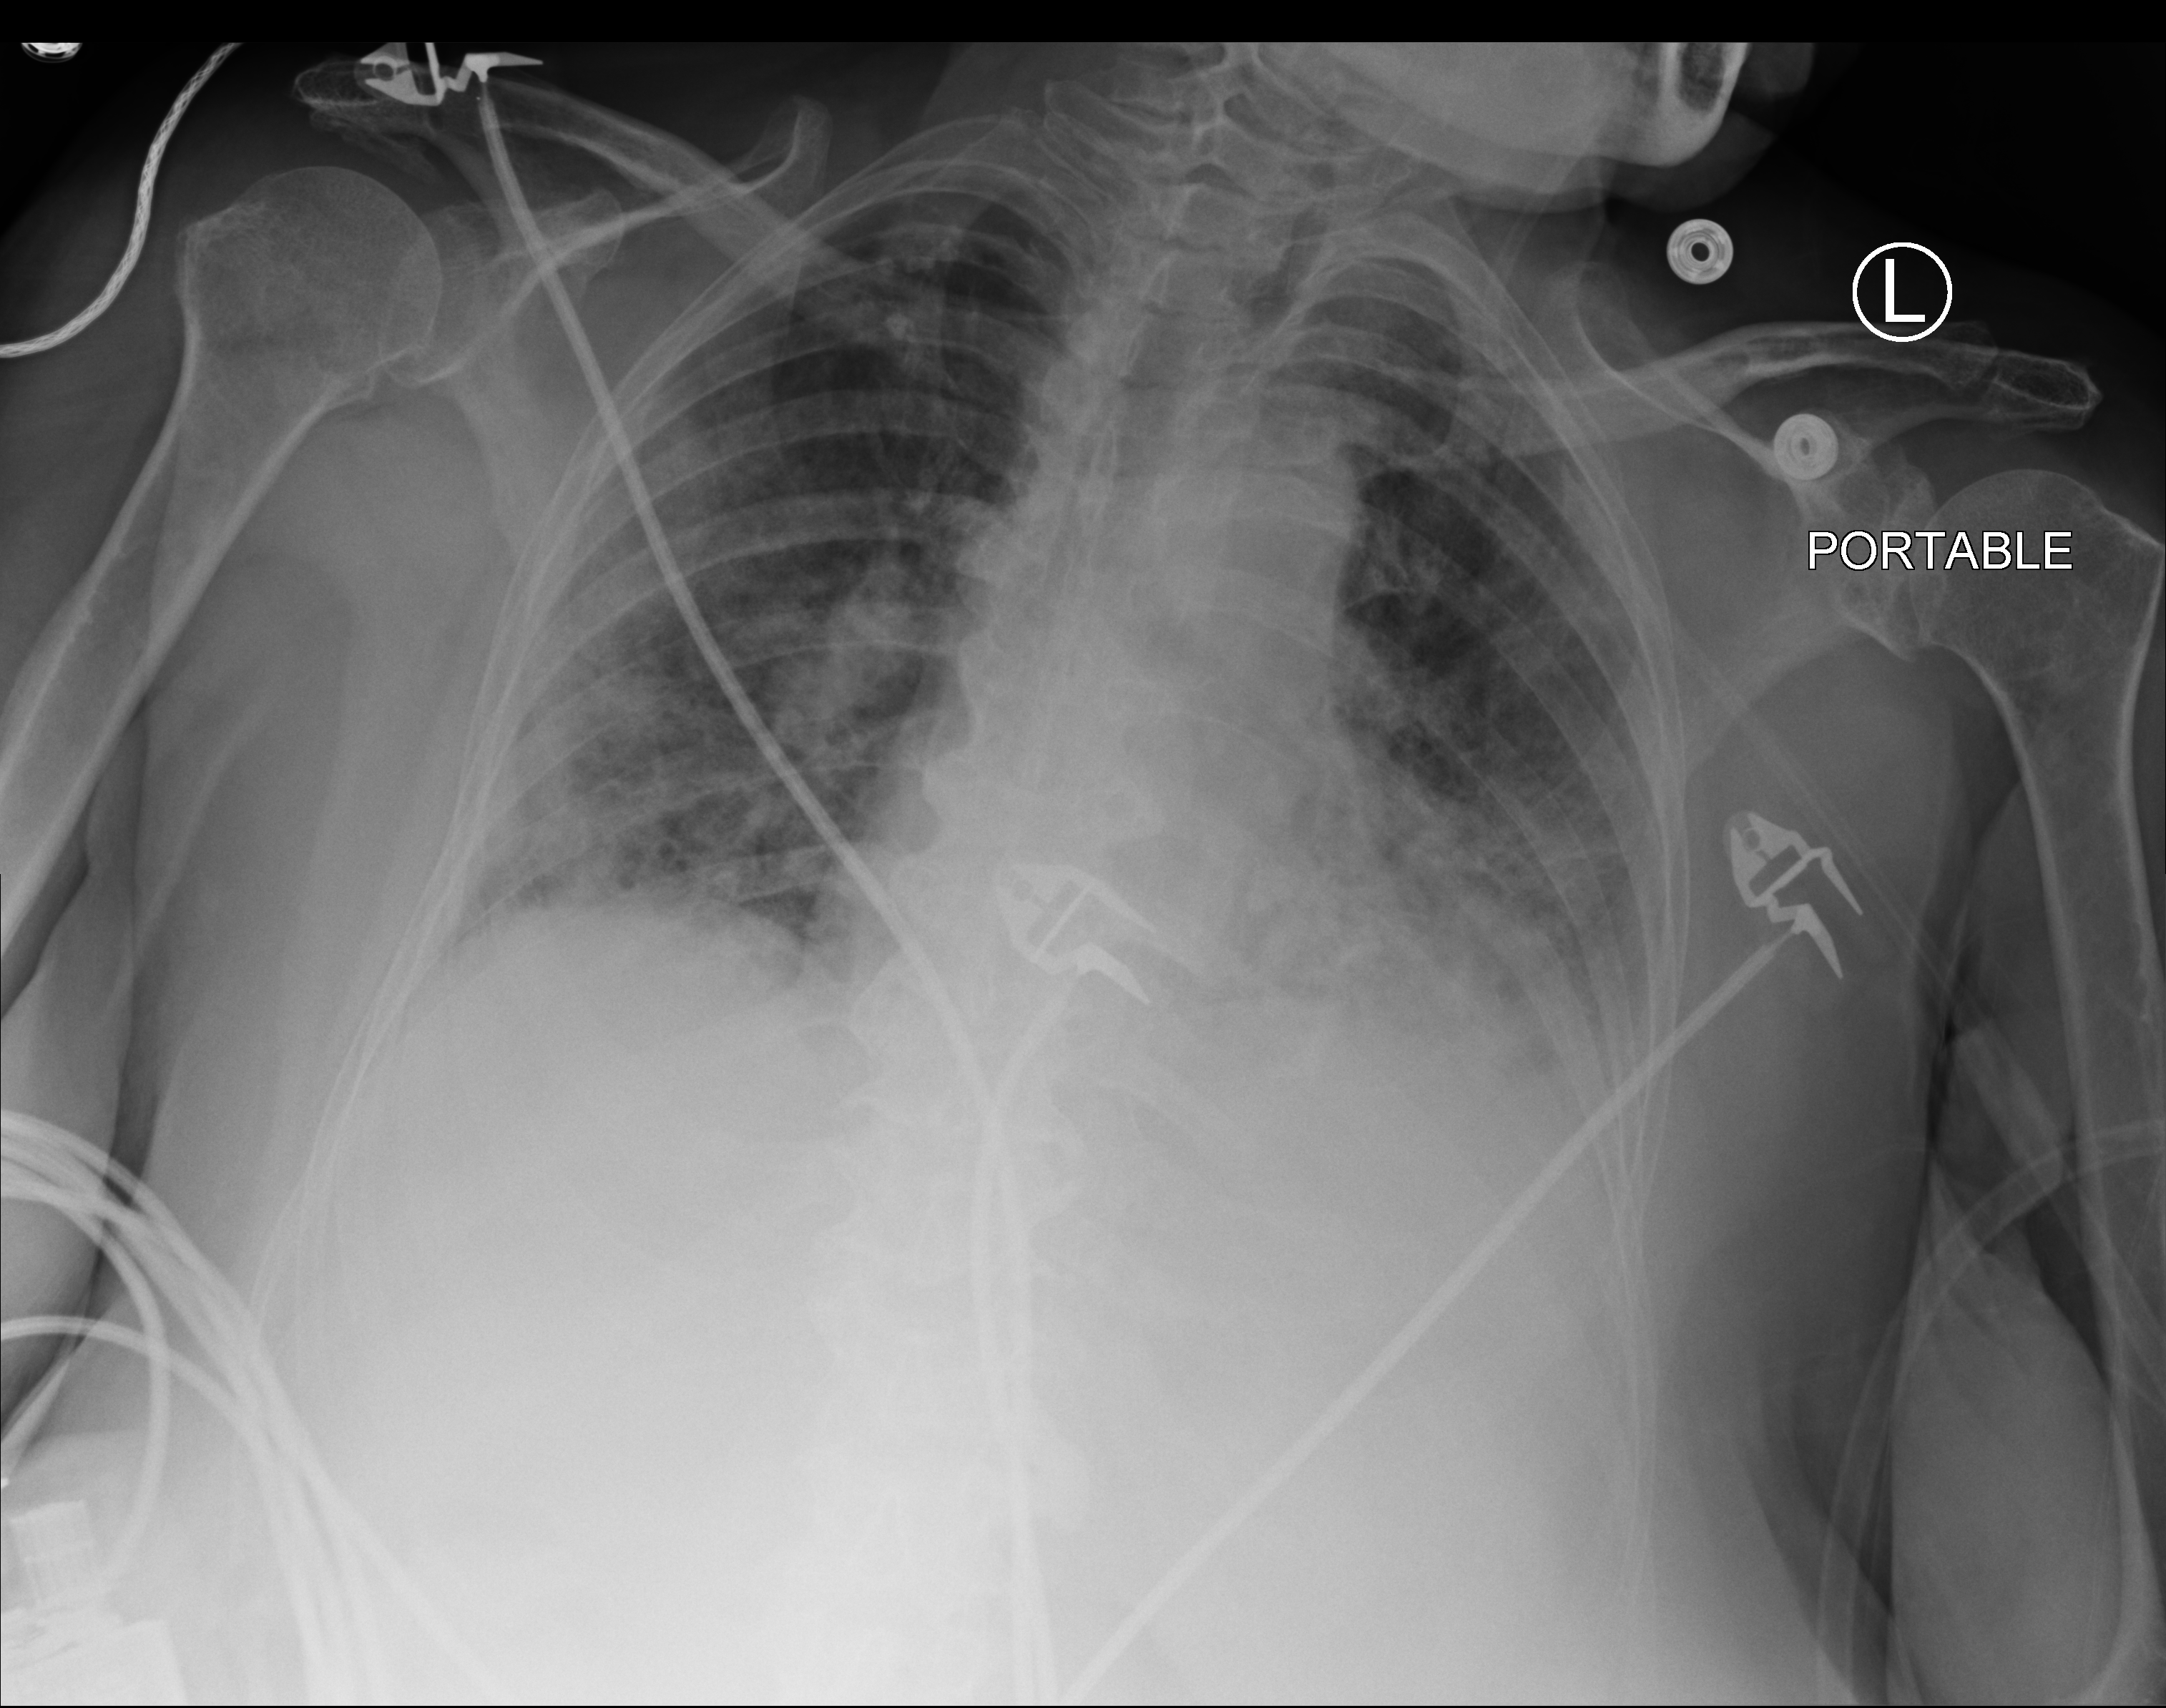
Bedside chest radiograph (computed radiography), anteroposterior (AP) projection. Female patient hospitalised with COVID-19, age 75–90 years.
Hospital-stay facts (about this admission, not read from this image; timing relative to this image not recorded):
- length of hospital stay: 37 days